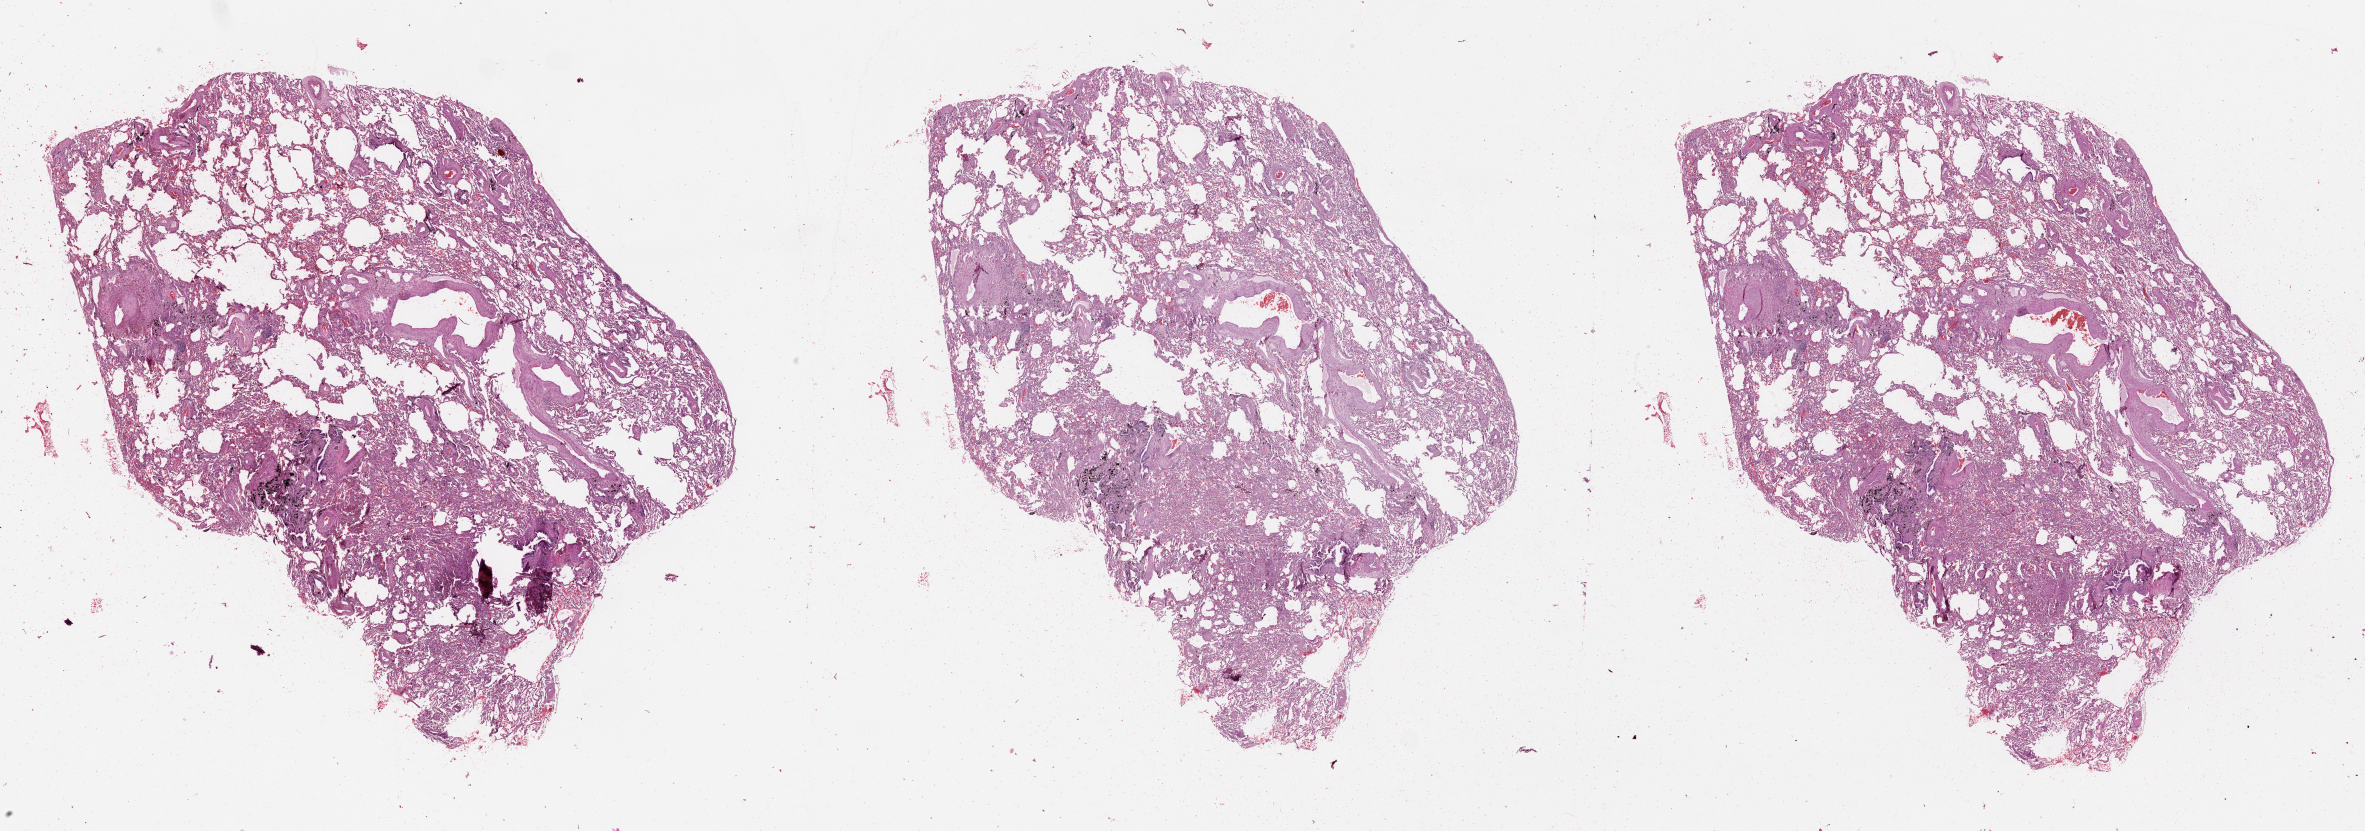
Hematoxylin and eosin (H&E) stained whole-slide image, shown as a low-resolution overview of the whole scanned area (about 38.1 x 13.4 mm); normal (non-tumour) tissue sample, lung. Patient: male, age 71 years.
• this section: normal (non-tumour) tissue from the same patient
• patient diagnosis (cohort enrolment): squamous cell carcinoma (lung)